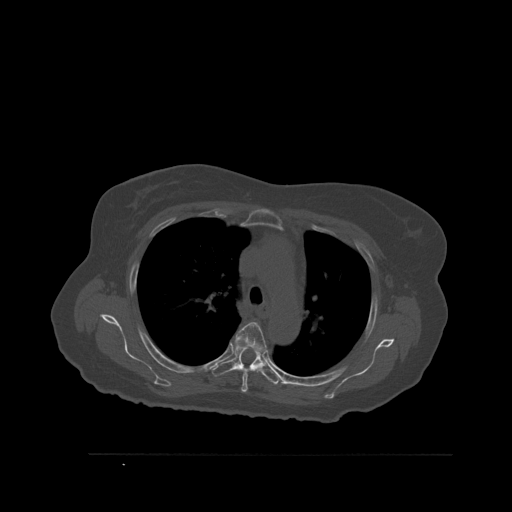
CT including the spine, one axial slice. Position 401 of 527 along the scan axis. Bone window (W 1800 / L 400 HU). 512 × 512 image matrix, field of view 470 × 470 mm. Patient: female, 73 years. From the clinical record (not read from this slice): primary cancer: breast.
Annotated regions visible in this slice (semi-automatically segmented with operator editing):
- T4 vertebra: bounding box <235,322,267,393> (left, top, right, bottom; pixels)
- T5 vertebra: <211,342,280,385>